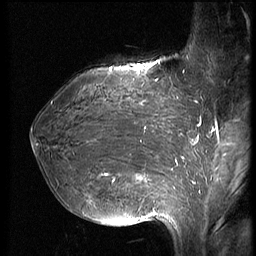
Breast MRI (dynamic contrast-enhanced), one sagittal slice; slice 25 of 66 in the series (ordered by position); dynamic contrast-enhanced series, image 2 of 3 at this slice position (ordered by acquisition); 1.5 T; TE 4.2 ms, TR 8.9 ms; 2.5 mm slice thickness; 256 × 256 image matrix, field of view 200 × 200 mm. Patient: female, 39 years. From the clinical record (not read from this slice): setting: breast cancer imaged before/during neoadjuvant chemotherapy; receptor status: HER2-positive.
Annotated regions visible in this slice (semi-automatically segmented with operator editing):
- analysis volume of interest (the breast-tissue region the enhancement analysis was run in; not a lesion): bounding box [x1, y1, x2, y2] px = [32, 75, 188, 218]
- tumour enhancement mask (voxels above the 140 % enhancement threshold inside the analysis volume of interest): [102, 81, 183, 213]